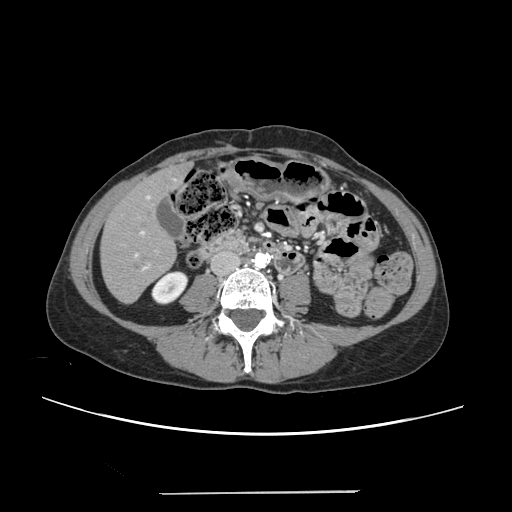
Contrast-enhanced abdominal CT, one axial slice; position 66 of 240 along the scan axis; intravenous contrast given; soft-tissue window (W 400 / L 40 HU); 1.25 mm slice thickness; 512 × 512 image matrix, field of view 371 × 371 mm. Female patient, age 60 years. Case-level facts recorded for this patient, not image findings: diagnosis: colorectal cancer liver metastases, imaged before liver resection; multiple liver metastases: no; largest metastasis: 1.5 cm; disease in both lobes: no.
Annotated regions visible in this slice (outlined manually by an expert reader):
- liver: bounding box [x1, y1, x2, y2] px = [102, 167, 187, 302]
- planned liver remnant (the part of the liver to remain after resection): [102, 171, 176, 302]
- portal vein (with intrahepatic branches): [134, 196, 158, 270]